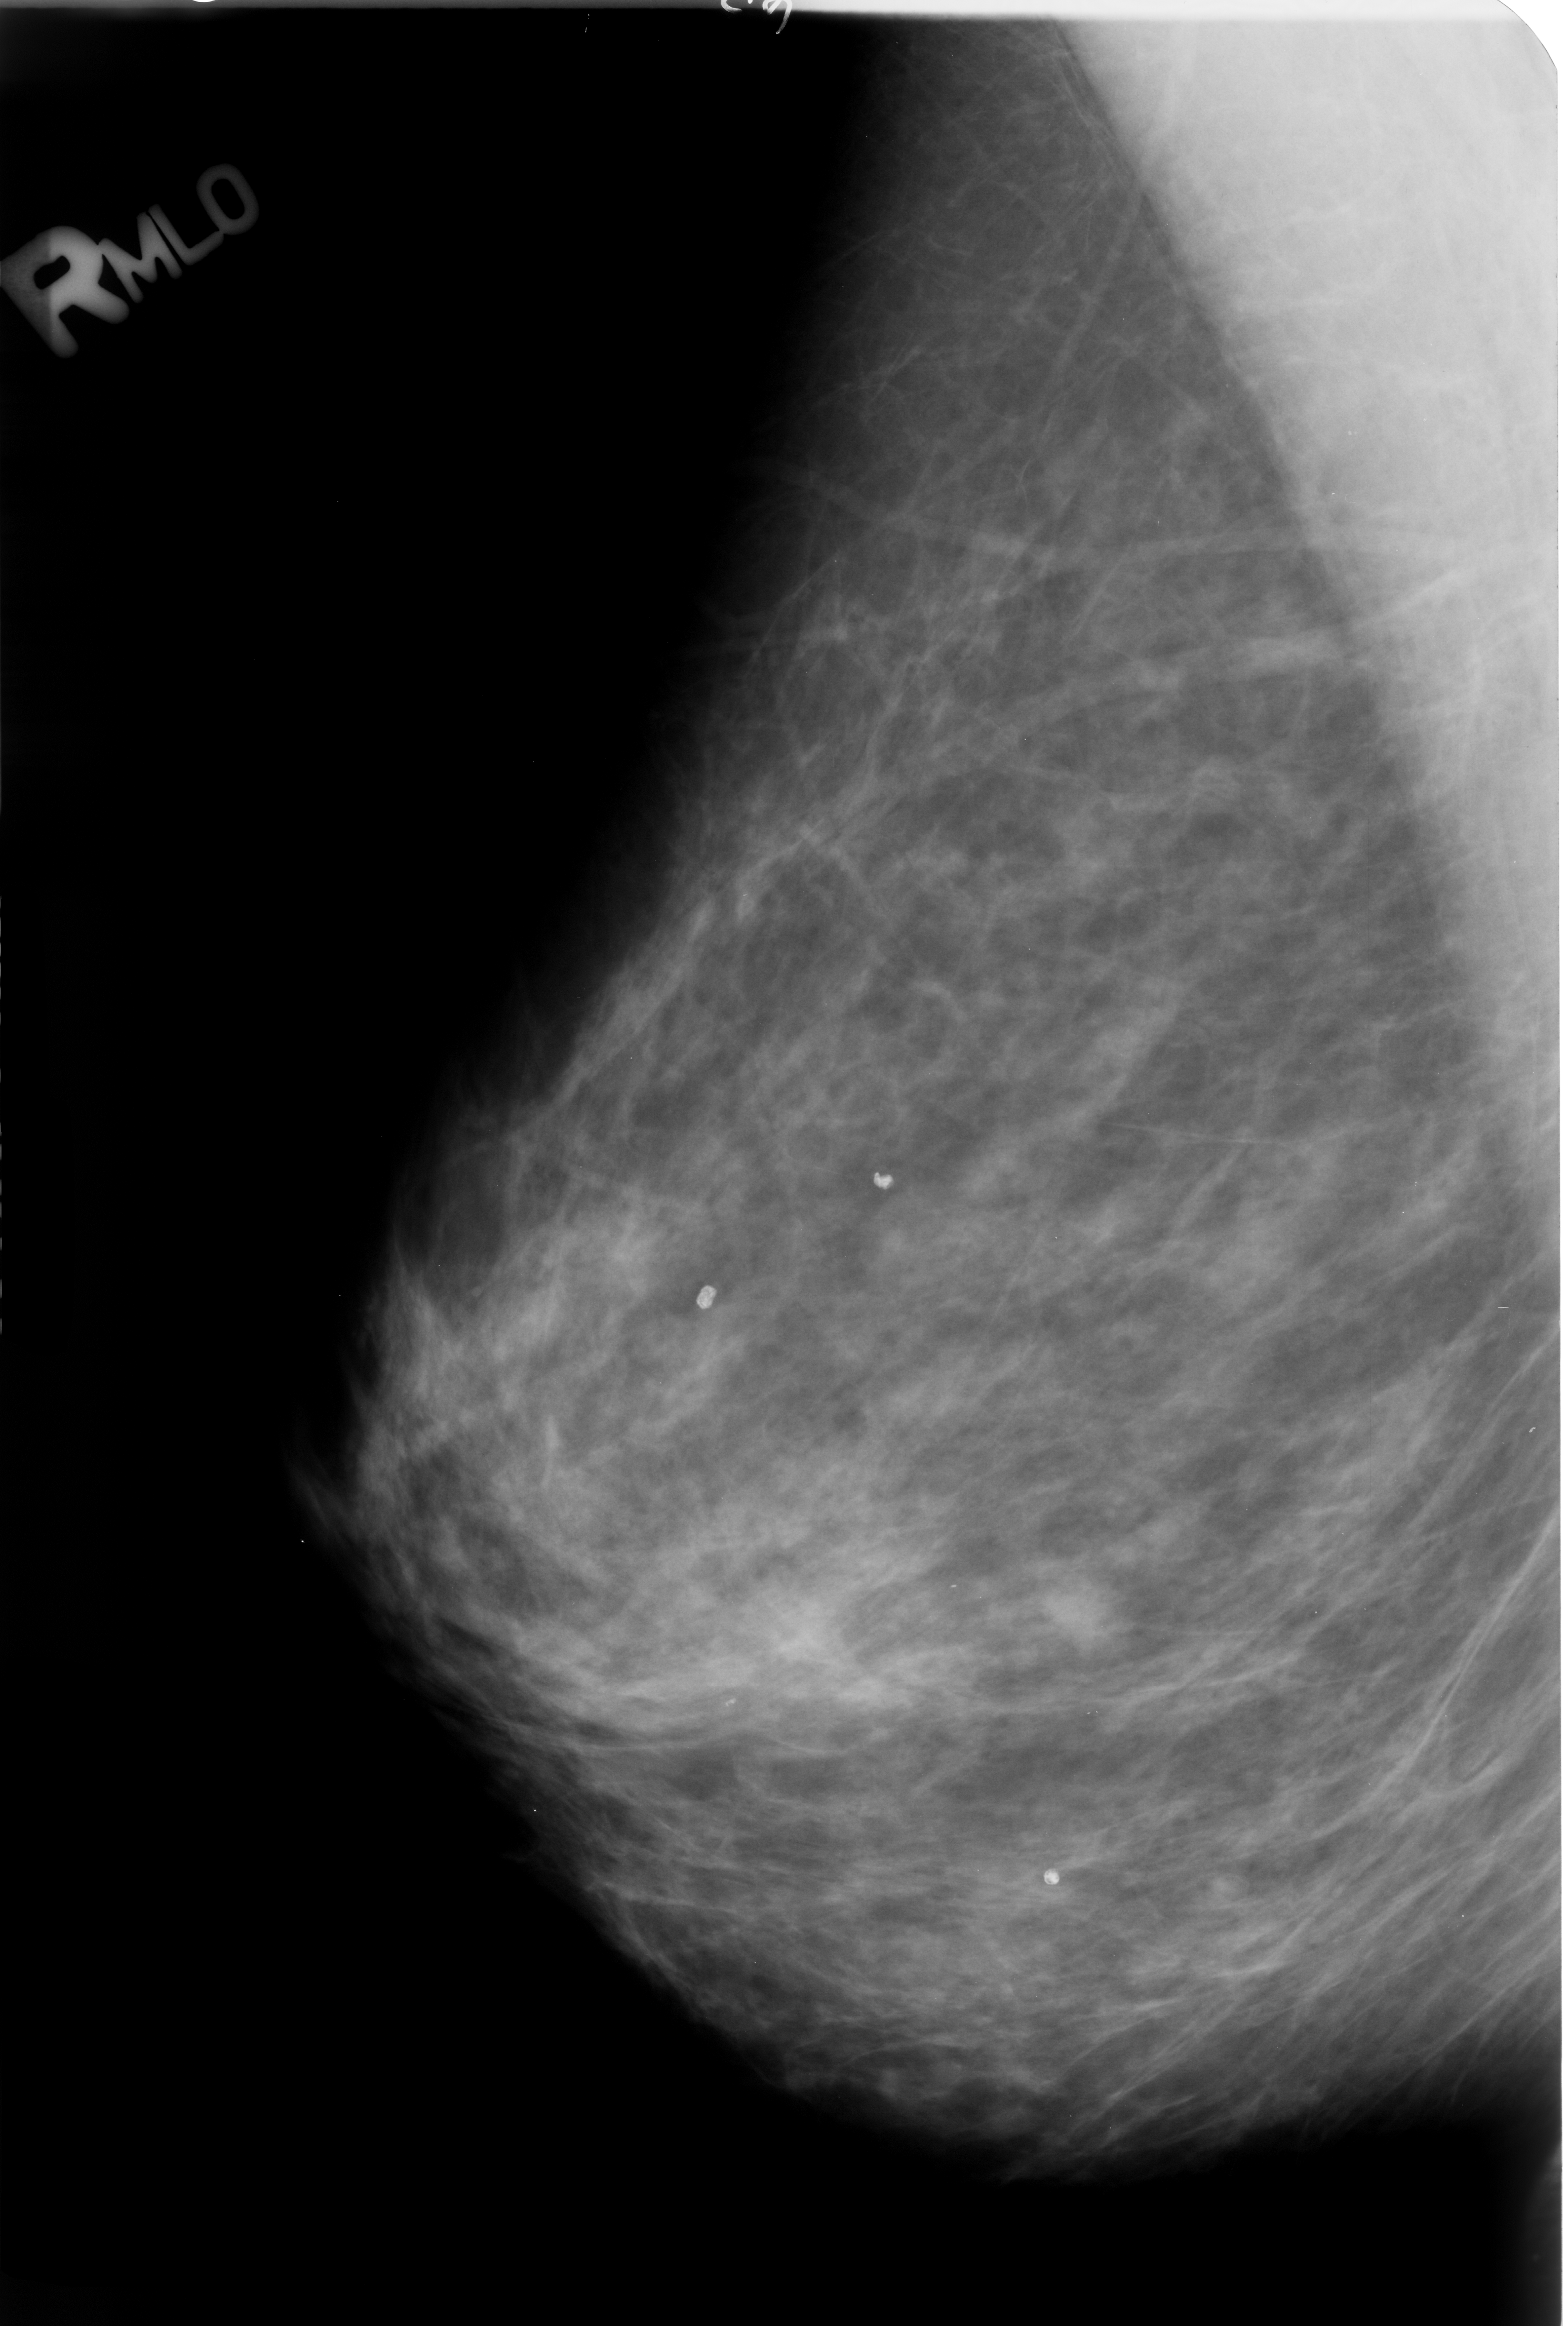
Digitized screen-film mammogram. Right breast. MLO view. Breast composition: scattered fibroglandular densities (BI-RADS density category 2 of 4). 1568 × 2326 image matrix.
Expert-marked regions of interest on this image (one box per marked abnormality):
- Finding 1 of 3: calcifications, morphology coarse / round and regular / lucent center; BI-RADS assessment category 2; subtlety rating 5 on a 1 (subtle) to 5 (obvious) scale; outcome (as recorded, no biopsy): benign without callback (not worked up further): bounding box (x1, y1, x2, y2) in pixels: (696, 1280, 722, 1318)
- Finding 2 of 3: calcifications, morphology coarse / round and regular / lucent center; BI-RADS assessment category 2; subtlety rating 5 on a 1 (subtle) to 5 (obvious) scale; outcome (as recorded, no biopsy): benign without callback (not worked up further): (871, 1163, 900, 1196)
- Finding 3 of 3: calcifications, morphology coarse / round and regular / lucent center; BI-RADS assessment category 2; subtlety rating 5 on a 1 (subtle) to 5 (obvious) scale; outcome (as recorded, no biopsy): benign without callback (not worked up further): (1029, 1864, 1067, 1893)